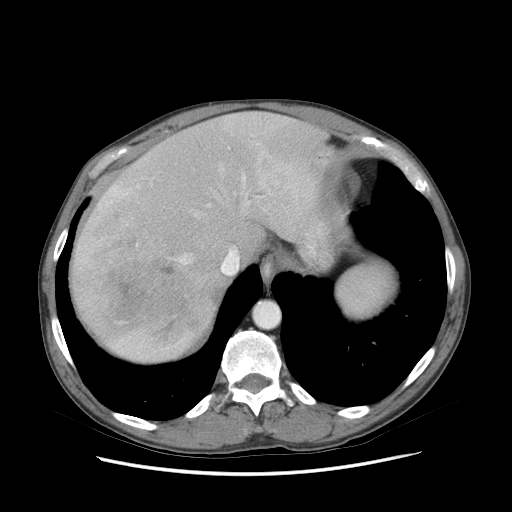
Contrast-enhanced abdominal CT (liver protocol), one axial slice; slice 64 of 89 in the series (ordered by position); soft-tissue window (W 400 / L 40 HU); 512 × 512 image matrix, field of view 380 × 380 mm. Case-level facts recorded for this patient, not image findings: diagnosis: hepatocellular carcinoma (patient treated with transarterial chemoembolisation; whether this scan precedes or follows treatment is not stated here); TNM stage (as recorded): Stage-IIIB; Child-Pugh class: A; tumour differentiation: moderately differentiated.
Annotated regions visible in this slice (semi-automatically segmented with operator editing):
- liver parenchyma outside the tumour (the mass and vessels are separate outlines, so this box may not span the whole liver): bounding box (x1, y1, x2, y2) in pixels: (70, 112, 342, 360)
- mass: (84, 206, 207, 339)
- liver vessels: (97, 176, 246, 349)